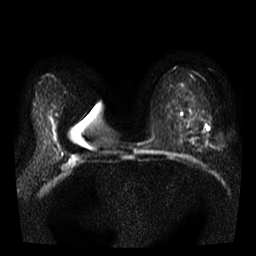
Breast MRI, one axial slice; position 22 of 38 along the scan axis; diffusion-weighted series; image 2 of 4 stored at this slice position (different b-values; order by instance number); 3 T; 256 × 256 image matrix, field of view 320 × 320 mm. Female patient.
Structures marked on this image (manually delineated by an expert):
- tumour on diffusion-weighted imaging: box from (x=207, y=127) to (x=210, y=131) px